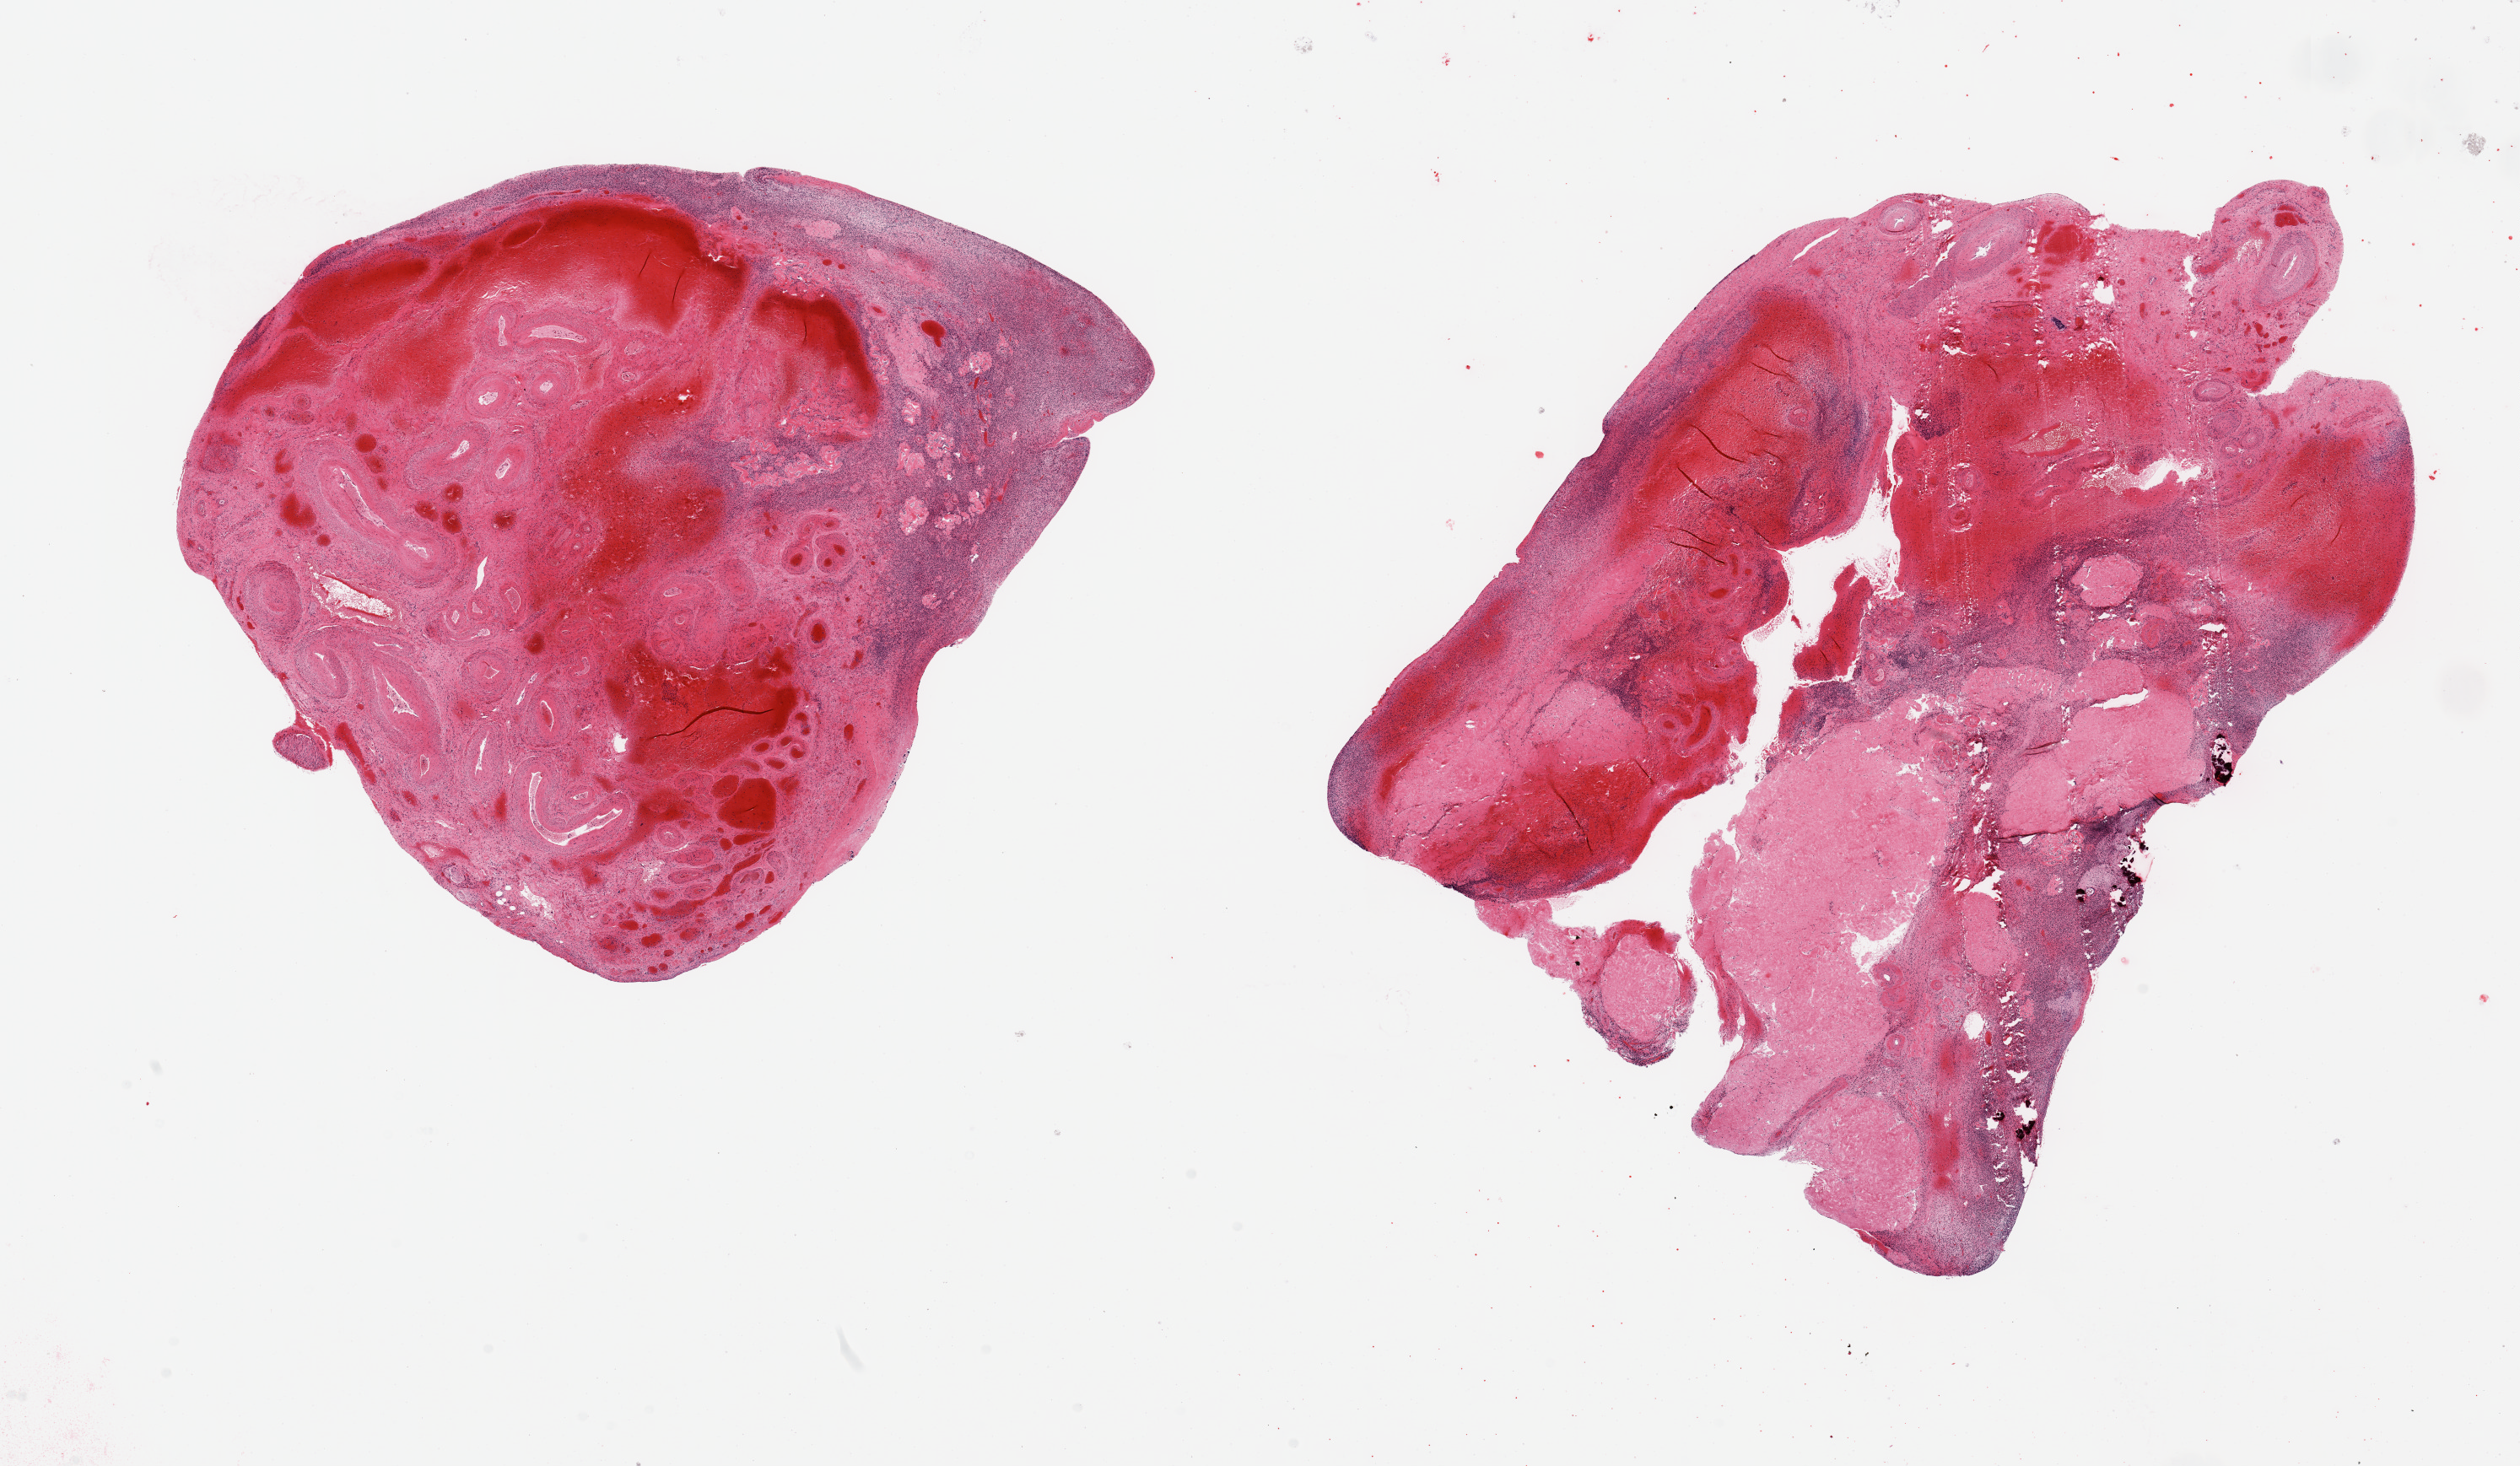
Digitized hematoxylin and eosin (H&E)-stained section — whole scanned area (about 23.6 x 13.7 mm) shown as a low-resolution overview. PAXgene-fixed paraffin-embedded (PFPE) section. Section of ovary (target tissue). Donor tissue sample. Female donor.
- reviewer comment on this tissue sample: 2 pieces; thin outer rim of parenchyma; core contains corpora albicantia and hemorrhagic stroma